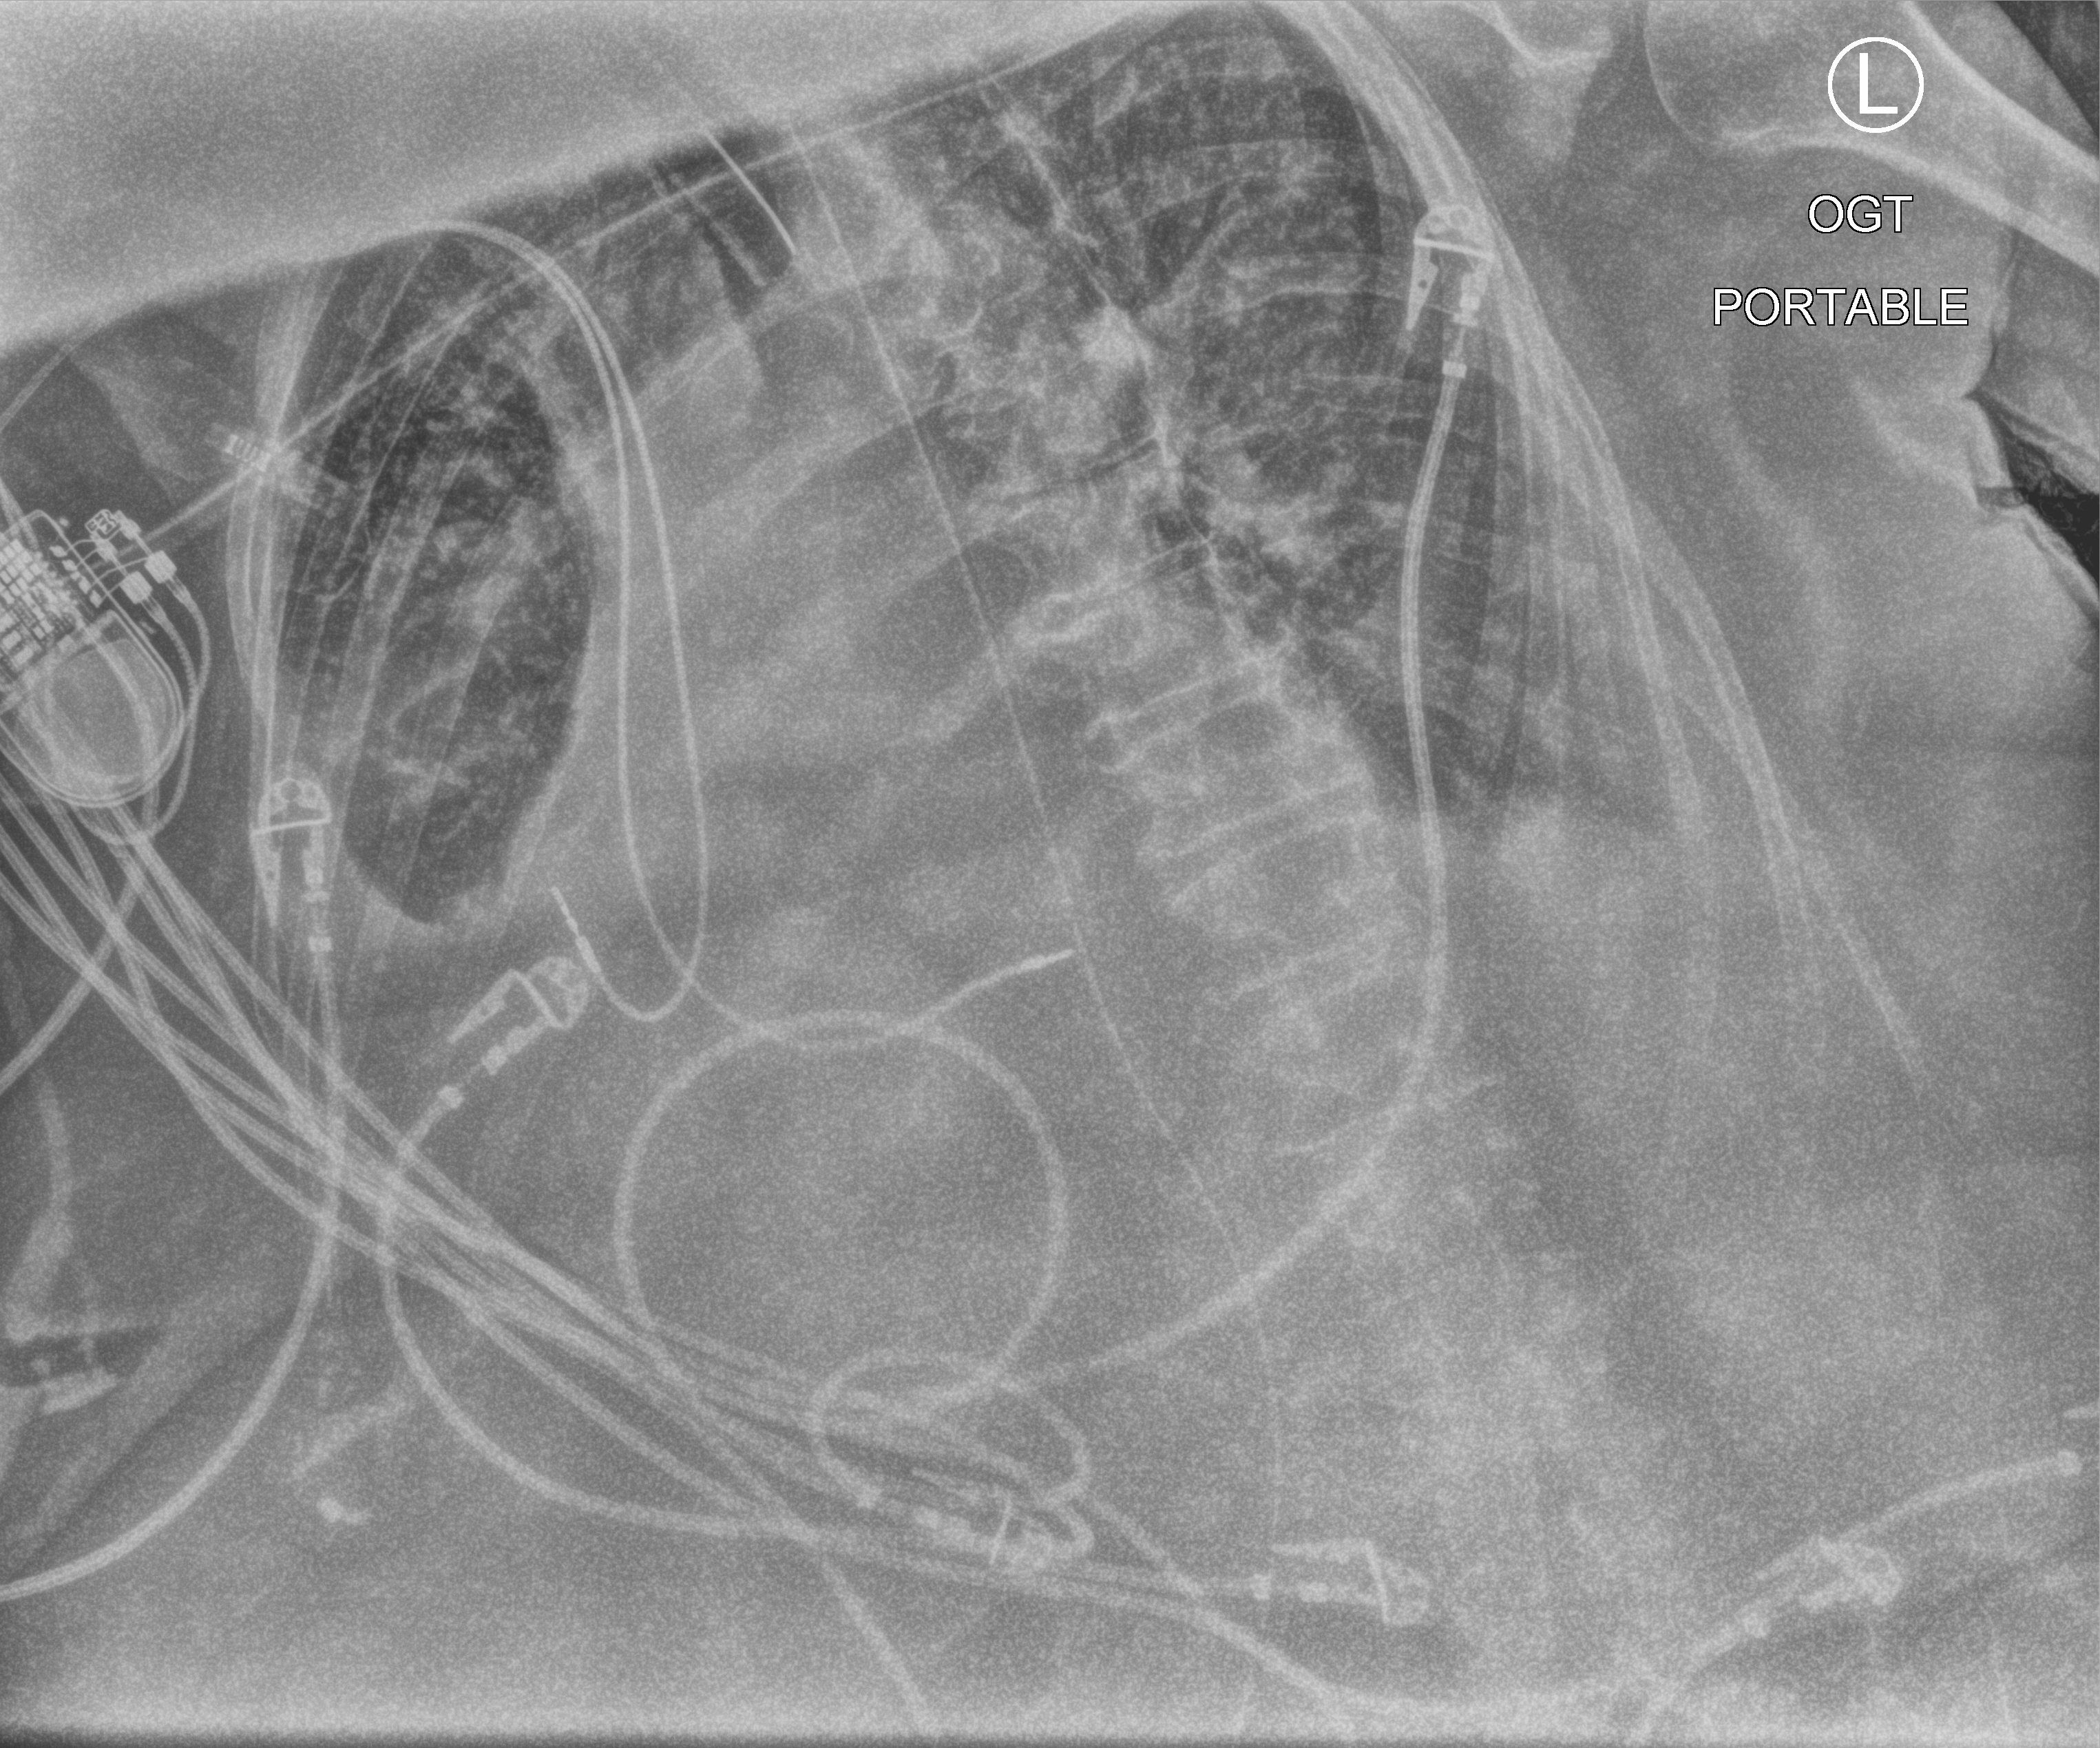
Chest X-ray (portable); anteroposterior (AP) projection. Patient hospitalised with COVID-19; female, aged 75–90 years.
From the hospital-stay record, not from the radiograph (when in the stay this image was taken is not recorded): other chronic lung disease (admission record): yes.